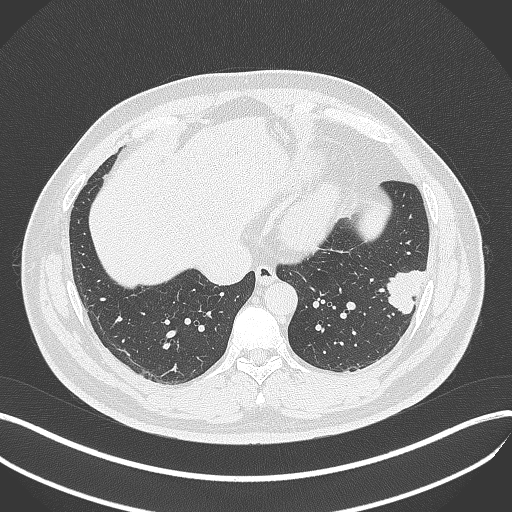
Chest CT, one axial slice. Slice 128 of 429 in the series (ordered by position). Lung window (W 1500 / L -600 HU). 512 × 512 image matrix. Male patient, age 39 years. From the clinical record (not read from this slice): clinical TNM (as recorded): T2a N0 M0; histopathological grade: G2-3.
Outlined on this slice (bounding box drawn by a radiologist):
- lung tumour (recorded histology: adenocarcinoma): bounding box [x1, y1, x2, y2] px = [378, 266, 426, 318]